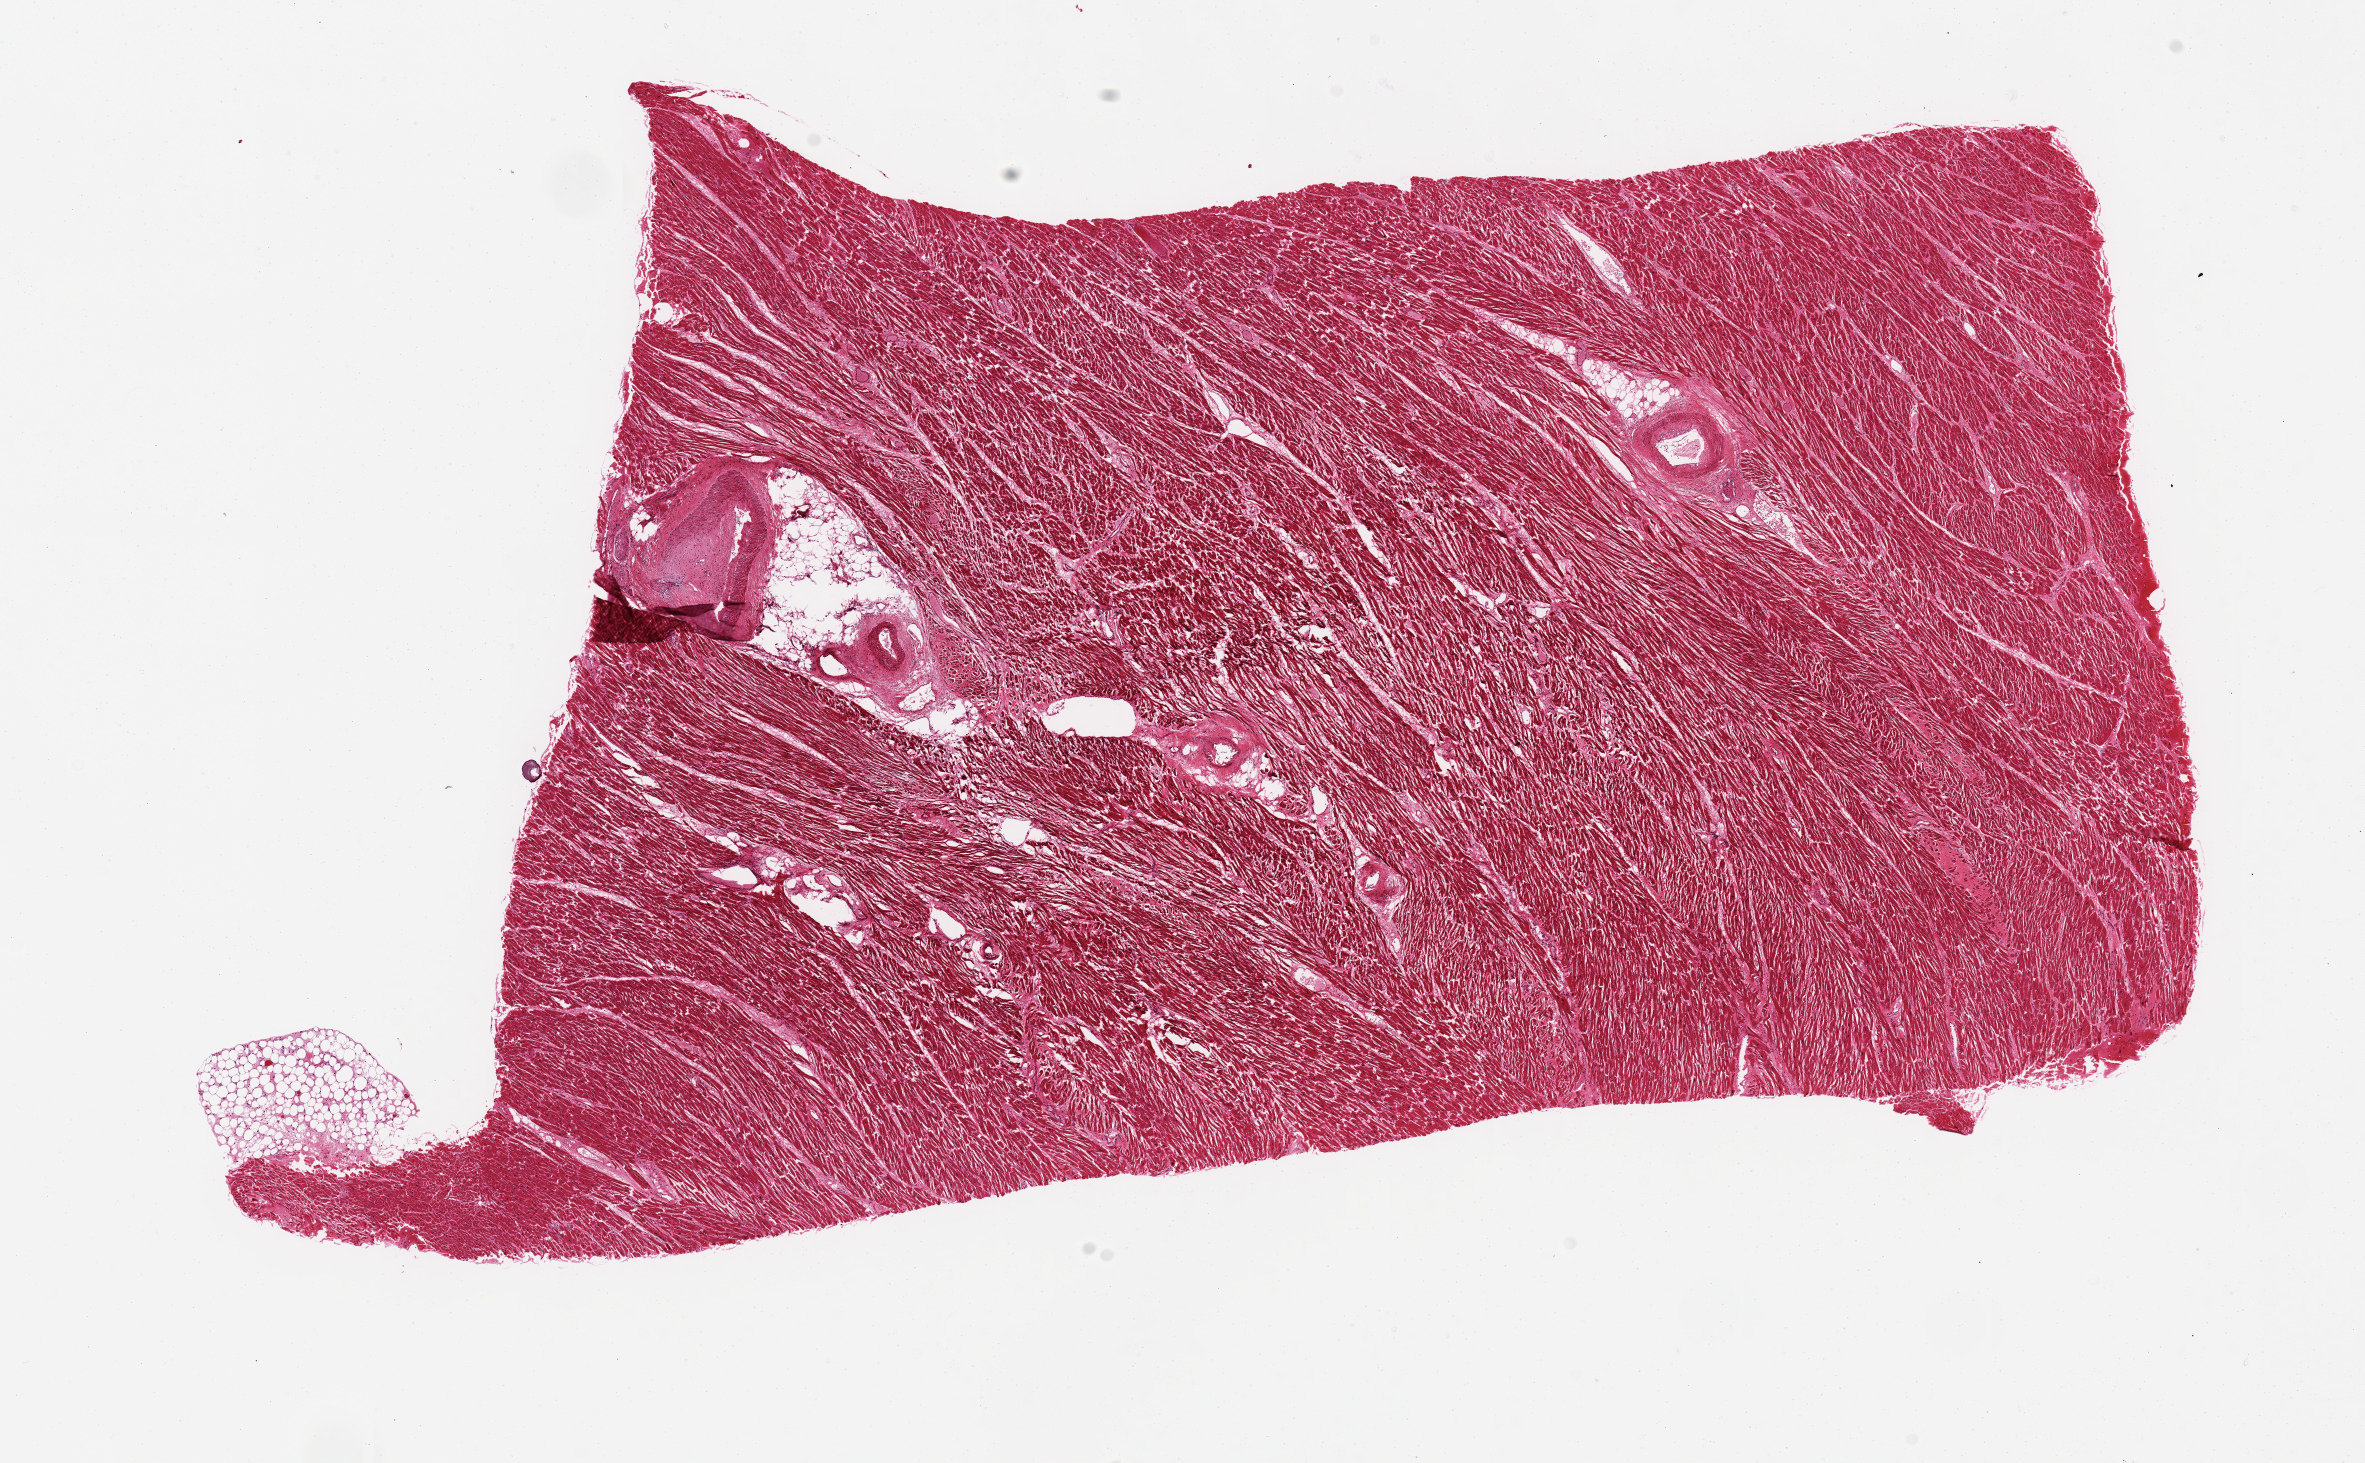
Whole-slide image, hematoxylin and eosin (H&E) stain — low-resolution overview of the scanned area, about 18.7 x 11.6 mm. PAXgene-fixed, paraffin-embedded tissue. Sampled site (target tissue): heart. Donor tissue sample. Donor sex: male.
Reviewer comment on this tissue sample: Minimal interstitial fibrosis.